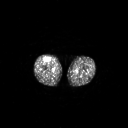
FDG PET of an extremity soft-tissue mass (from a PET/CT study), one axial slice. Position 244 of 311 along the scan axis. 3.27 mm slice thickness. 128 × 128 image matrix. Patient: male, 56 years. From the clinical record (not read from this slice): histological type: pleiomorphic leiomyosarcoma; grade: intermediate; site of the primary tumour: right thigh.
Outlined on this slice (expert contour drawn on MRI and transferred to this co-registered scan by the dataset authors):
- gross tumour volume including surrounding oedema: bounding box <44,57,51,62> (left, top, right, bottom; pixels)